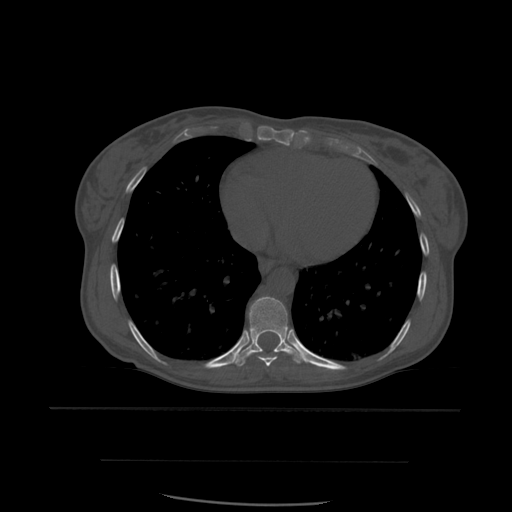
CT including the spine, one axial slice; slice 344 of 574 in the series (ordered by position); bone window (W 1800 / L 400 HU); 1.25 mm slice thickness; 512 × 512 image matrix. Patient age 48 years. From the clinical record (not read from this slice): primary cancer: lung; vertebrae with lytic lesions (as recorded): T11.
Annotated regions visible in this slice (semi-automatic segmentation, software-assisted and operator-edited):
- T8 vertebra: bounding box [x1, y1, x2, y2] px = [255, 351, 279, 367]
- T9 vertebra: [232, 297, 310, 367]